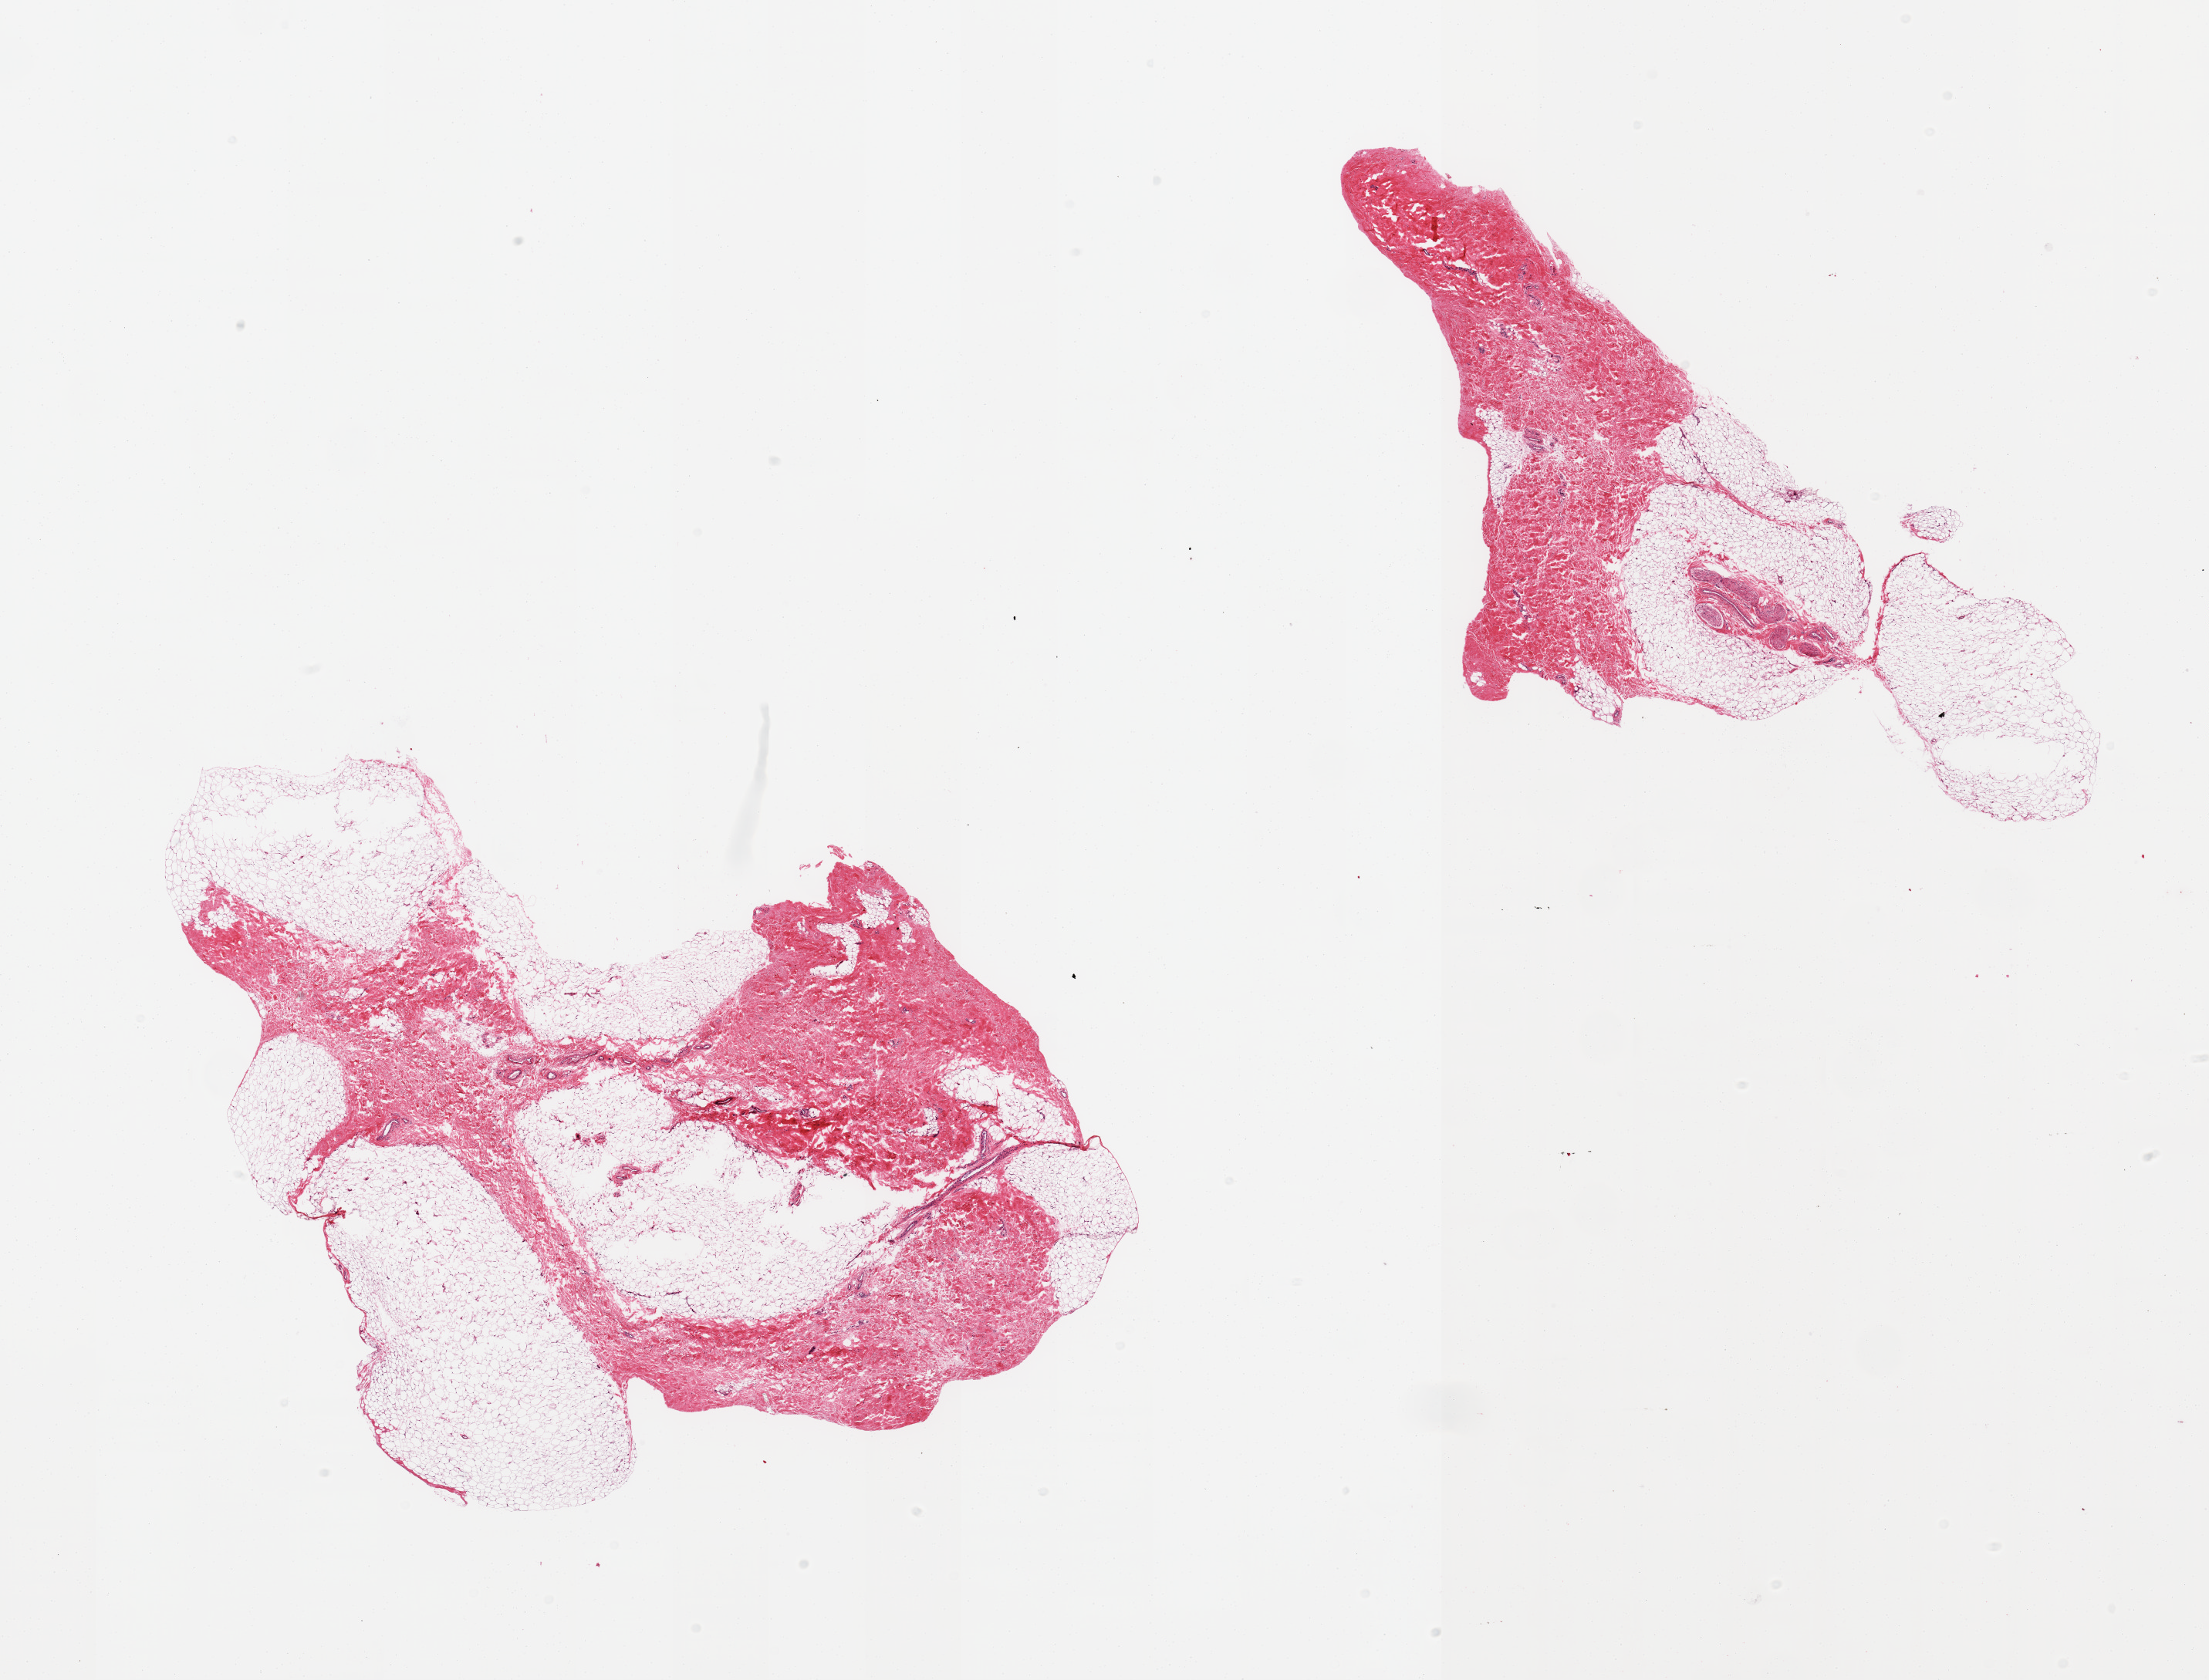
H&E whole-slide image, brightfield — a low-resolution overview of the entire scanned area, about 22.6 x 17.2 mm; PAXgene-fixed paraffin-embedded (PFPE) section; target tissue: breast; tissue donor sample.
Pathologist's review note for this sample: 2 pieces, gynecomastoid stromal hyperplasia; focal peripheral nerve/vascular elements.